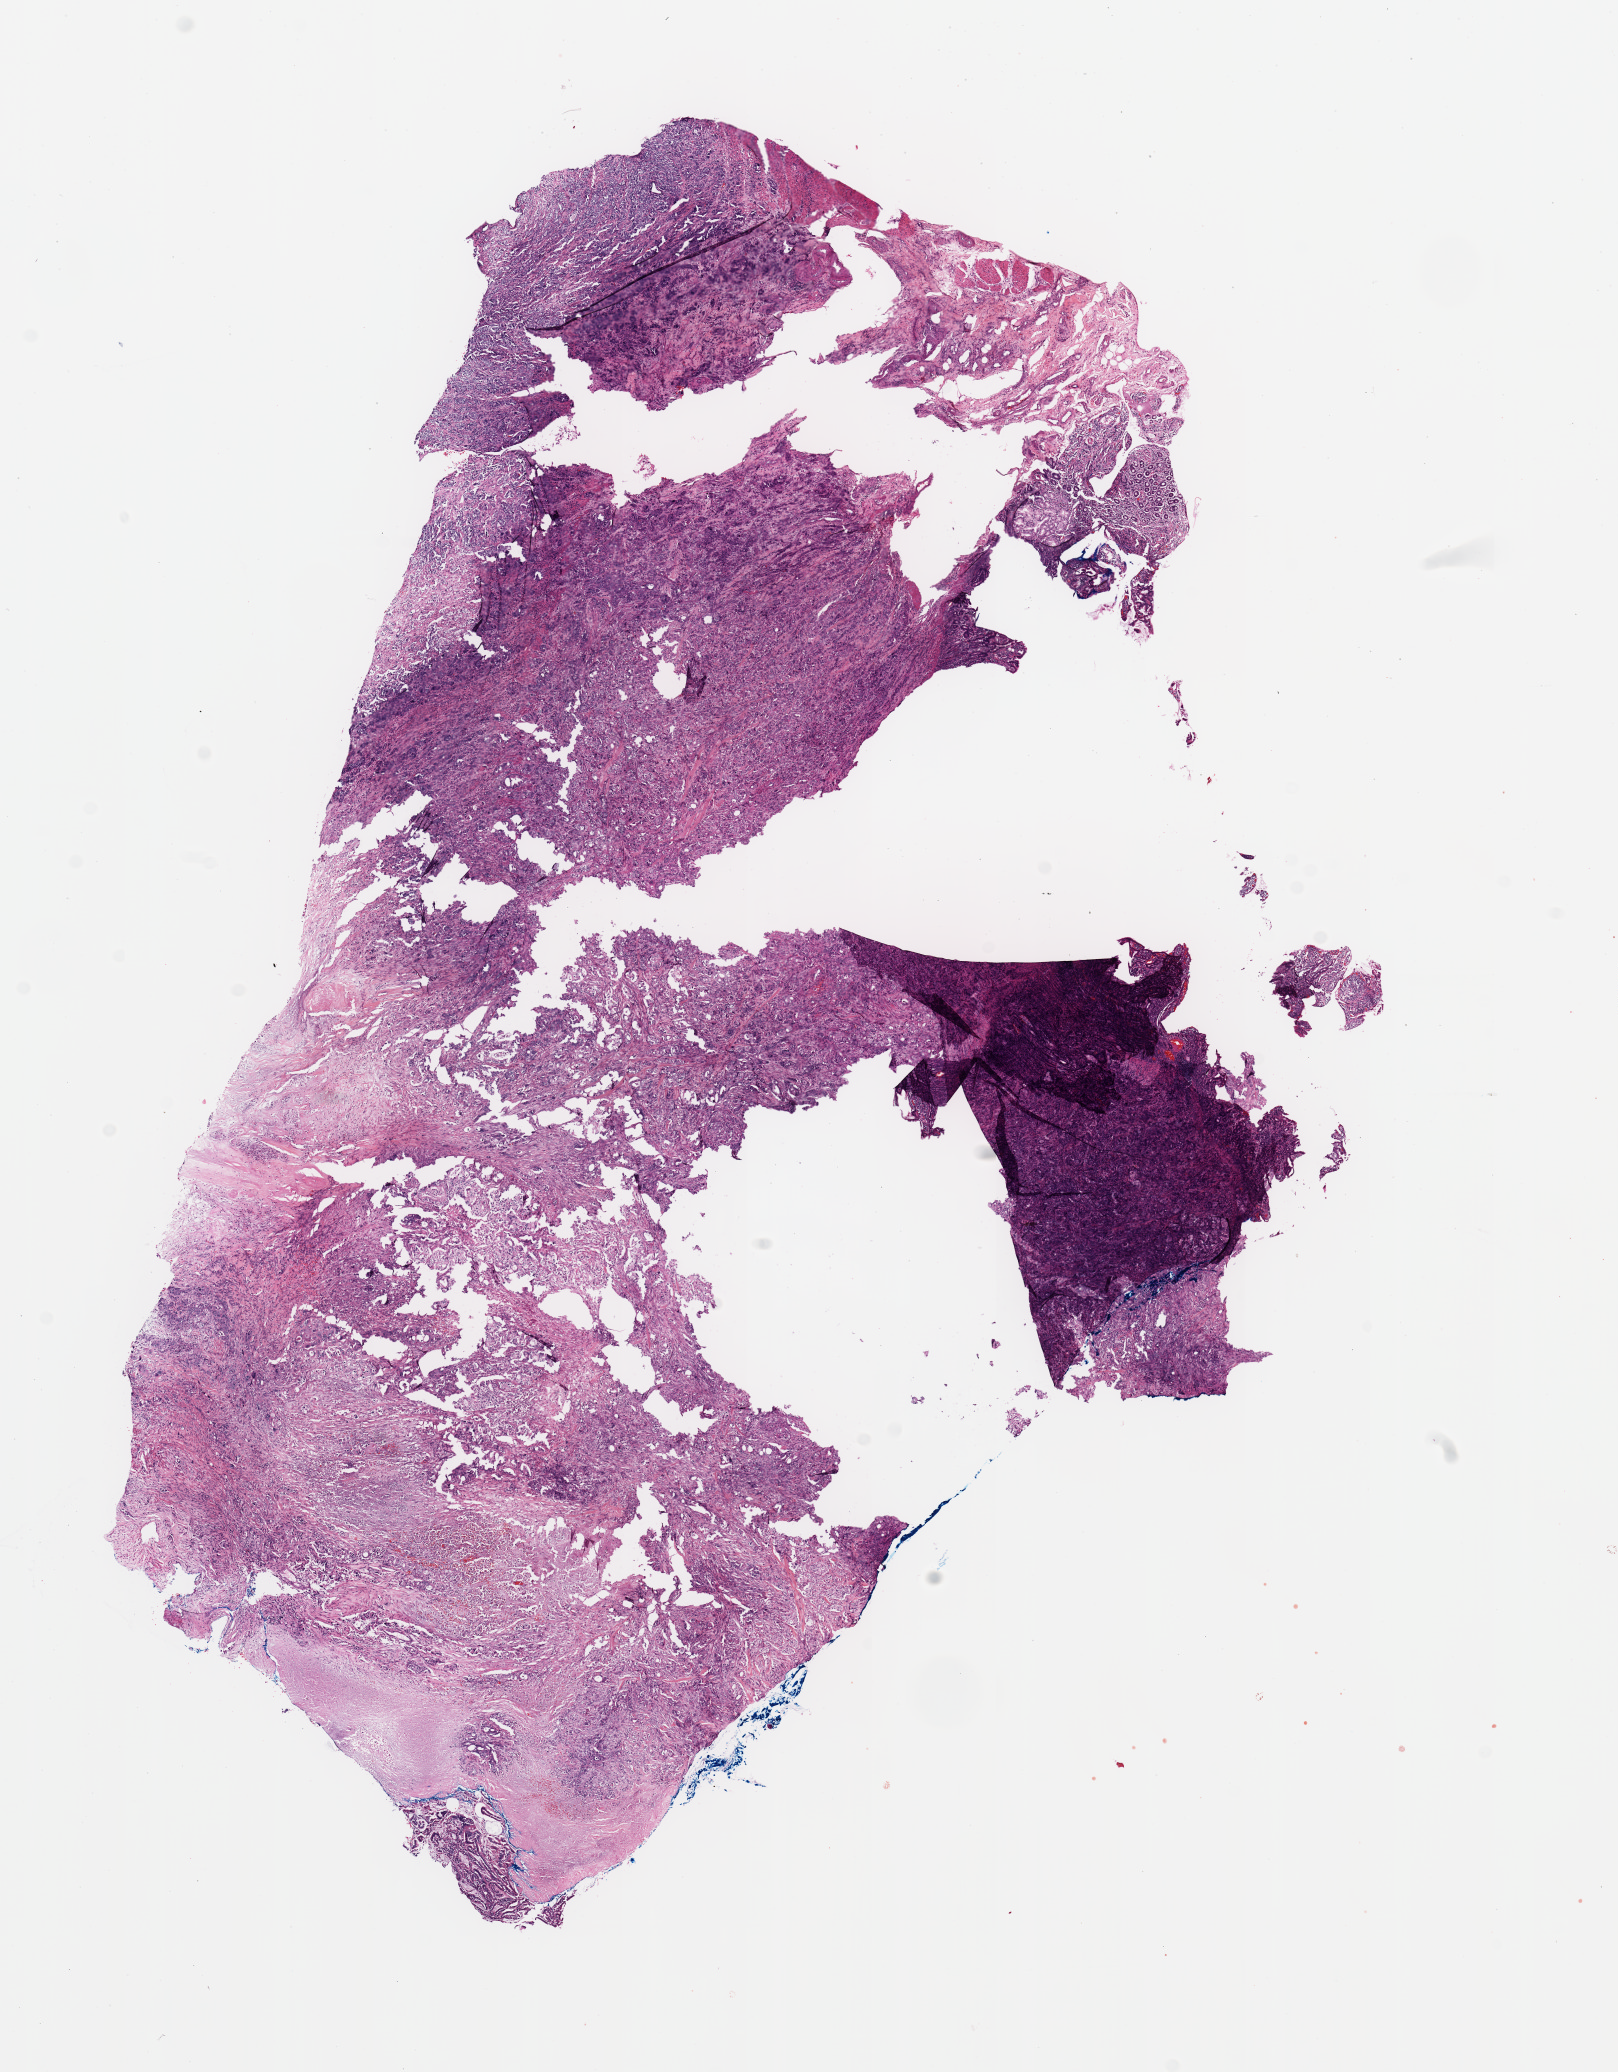
Digitized H&E tissue section (whole slide), a low-resolution overview of the entire scanned area, about 12.8 x 16.4 mm. Tumour tissue sample, sampled site: pancreas. Patient: female, age 52 years. Histologic grade: G3 (poorly differentiated). Composition of this section per pathologist review: tumour nuclei 80%, necrosis 10%.
Primary tumour site (as recorded): head. AJCC pathologic stage: IIB. Diagnosis: Infiltrating duct carcinoma, NOS.